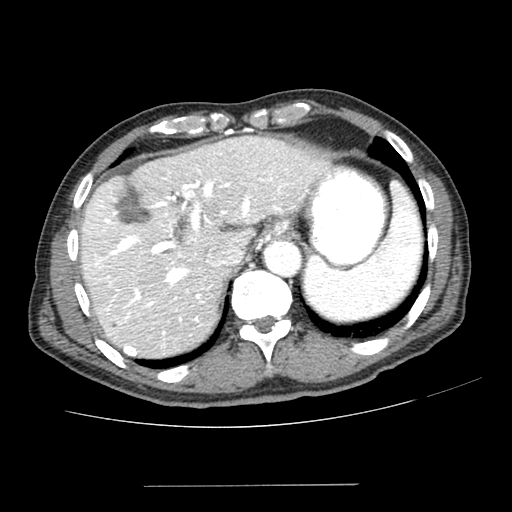
Contrast-enhanced abdominal CT (liver protocol), one axial slice; position 167 of 187 along the scan axis; reconstruction kernel SOFT; one of 2 acquisitions stored at this slice position; soft-tissue window (W 400 / L 40 HU); 512 × 512 image matrix, field of view 360 × 360 mm. From the clinical record (not read from this slice): diagnosis: hepatocellular carcinoma (patient treated with transarterial chemoembolisation; whether this scan precedes or follows treatment is not stated here); TNM stage (as recorded): Stage-I; Child-Pugh class: A; tumour differentiation: poorly differentiated; tumour nodularity: uninodular.
Annotated regions visible in this slice (semi-automatic segmentation, software-assisted and operator-edited):
- liver parenchyma outside the tumour (the mass and vessels are separate outlines, so this box may not span the whole liver): bounding box [x1, y1, x2, y2] px = [80, 136, 332, 358]
- liver vessels: [94, 164, 293, 351]